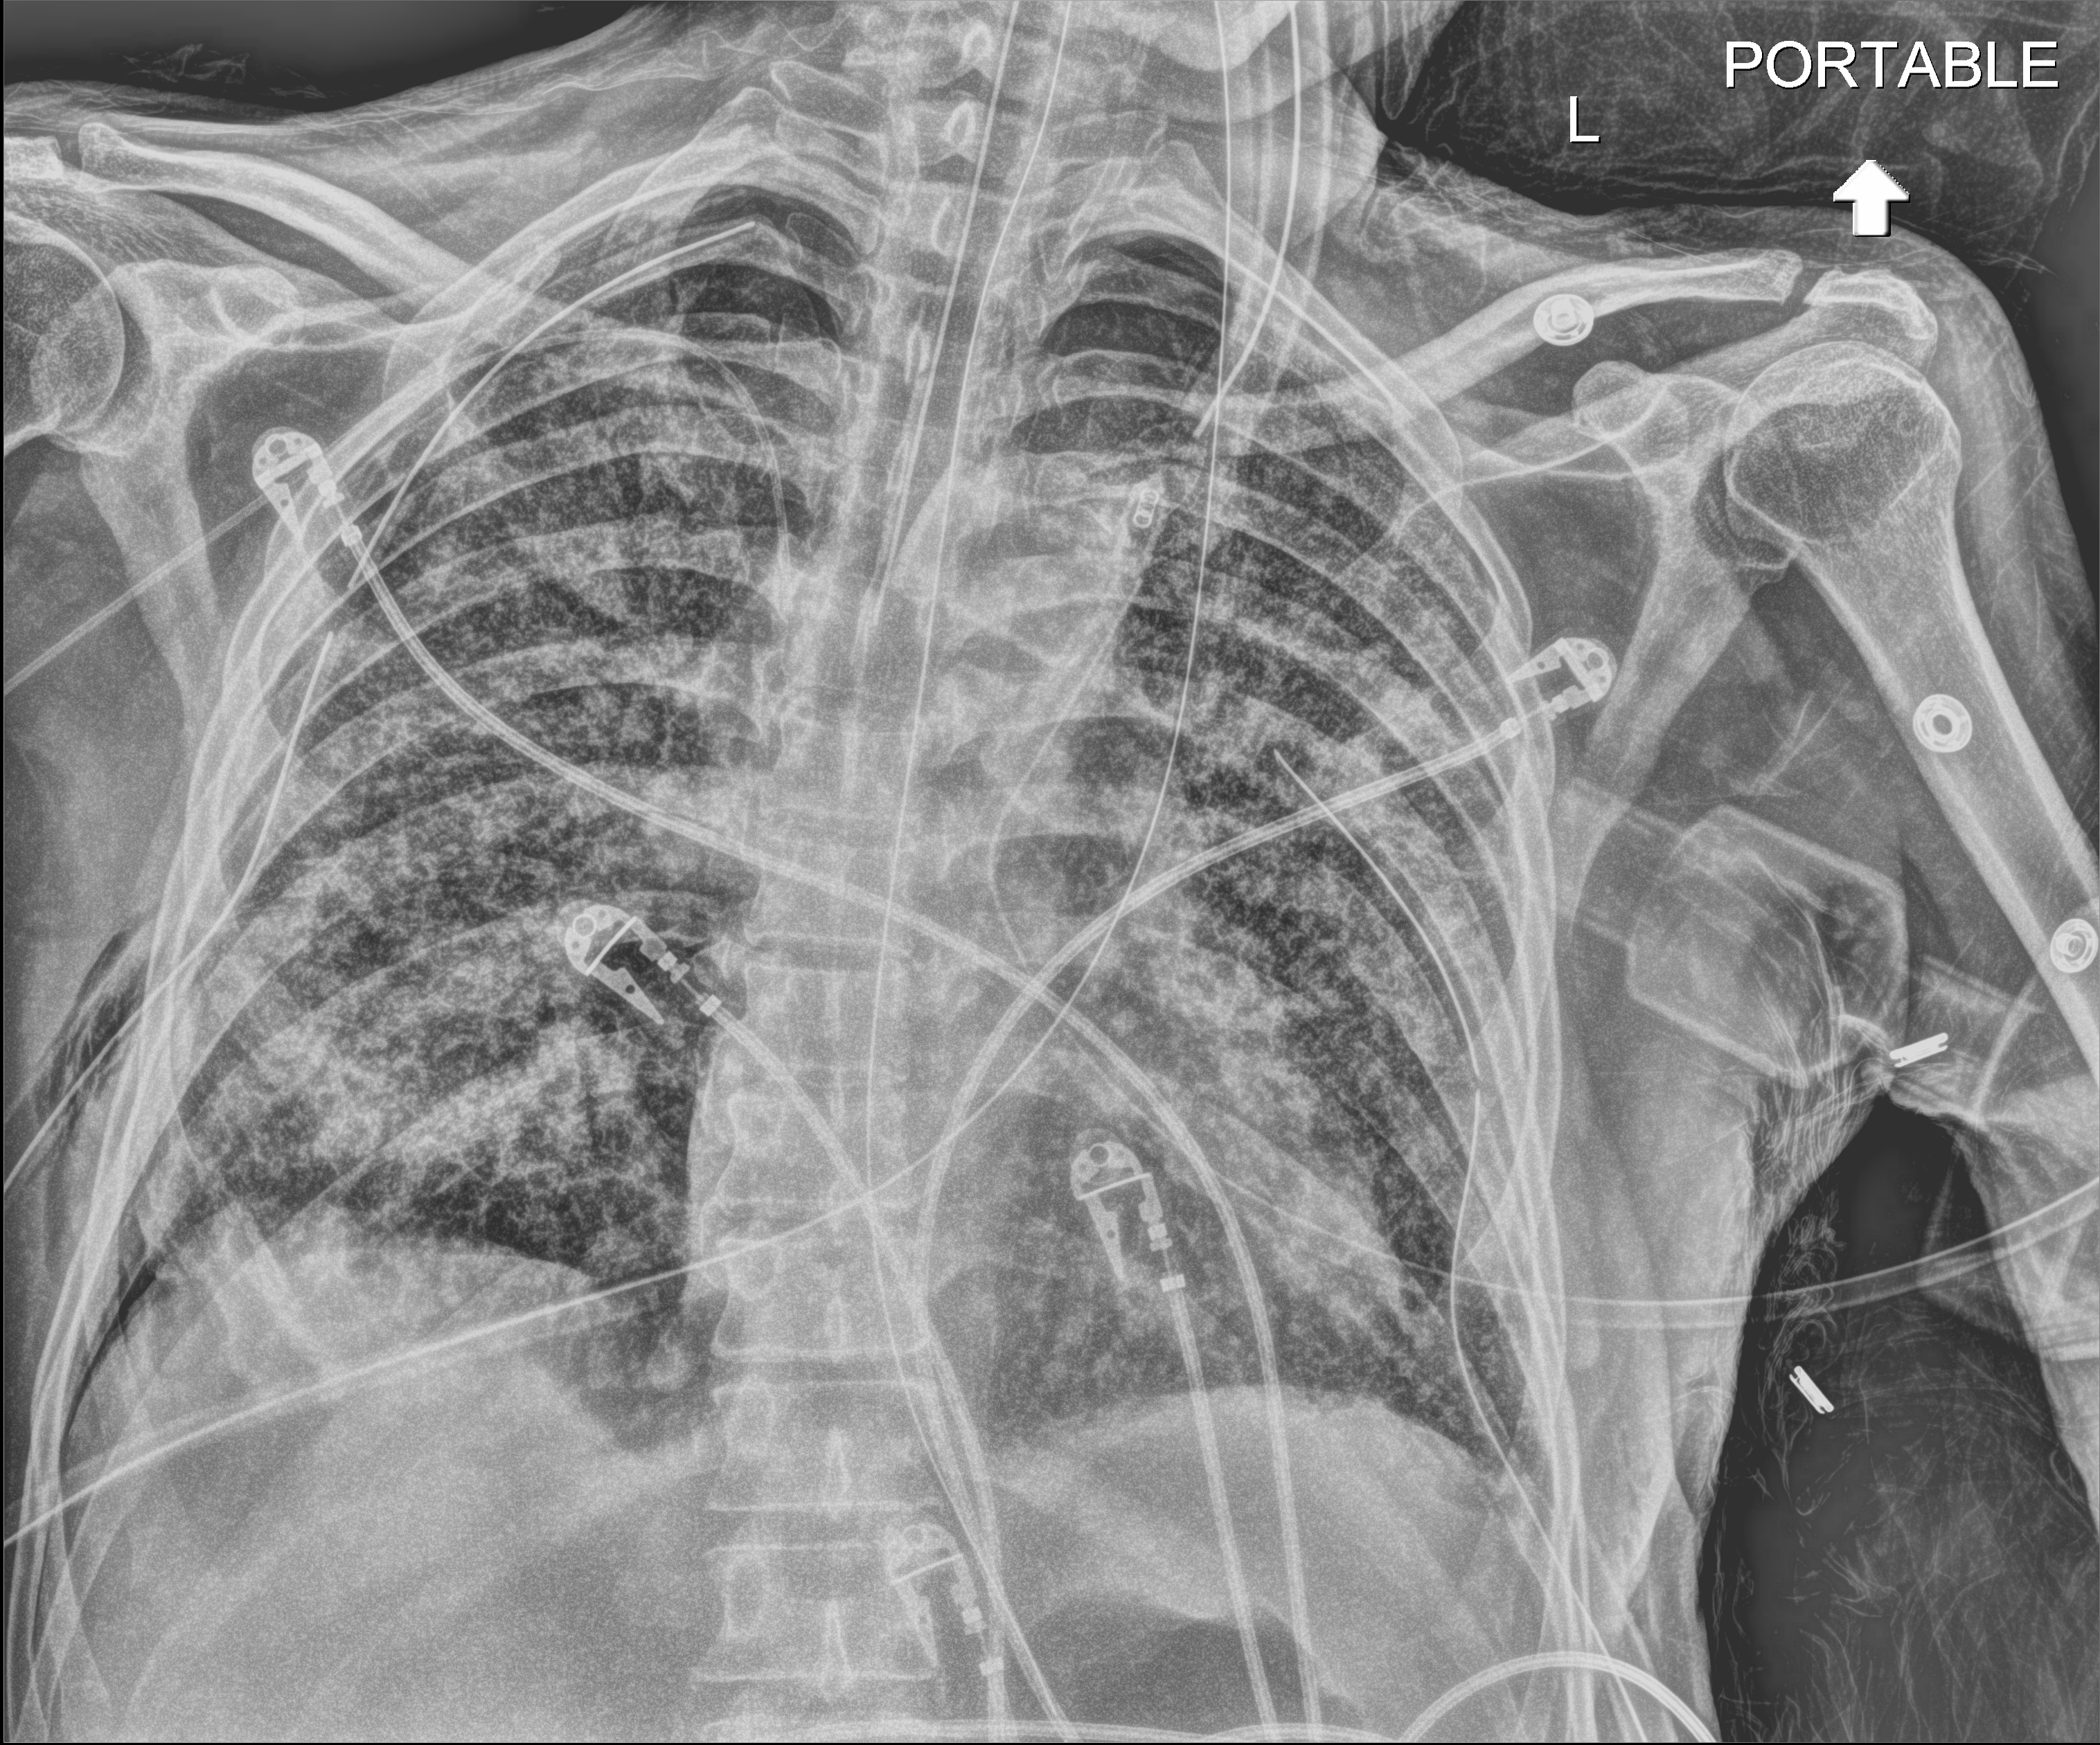
Bedside chest radiograph (digital radiography); anteroposterior (AP) projection. Patient hospitalised with COVID-19; male, aged 60–74 years.
Admission-level facts for this patient (not findings on this image; timing relative to this image not recorded): admitted to intensive care during this hospital stay: yes.